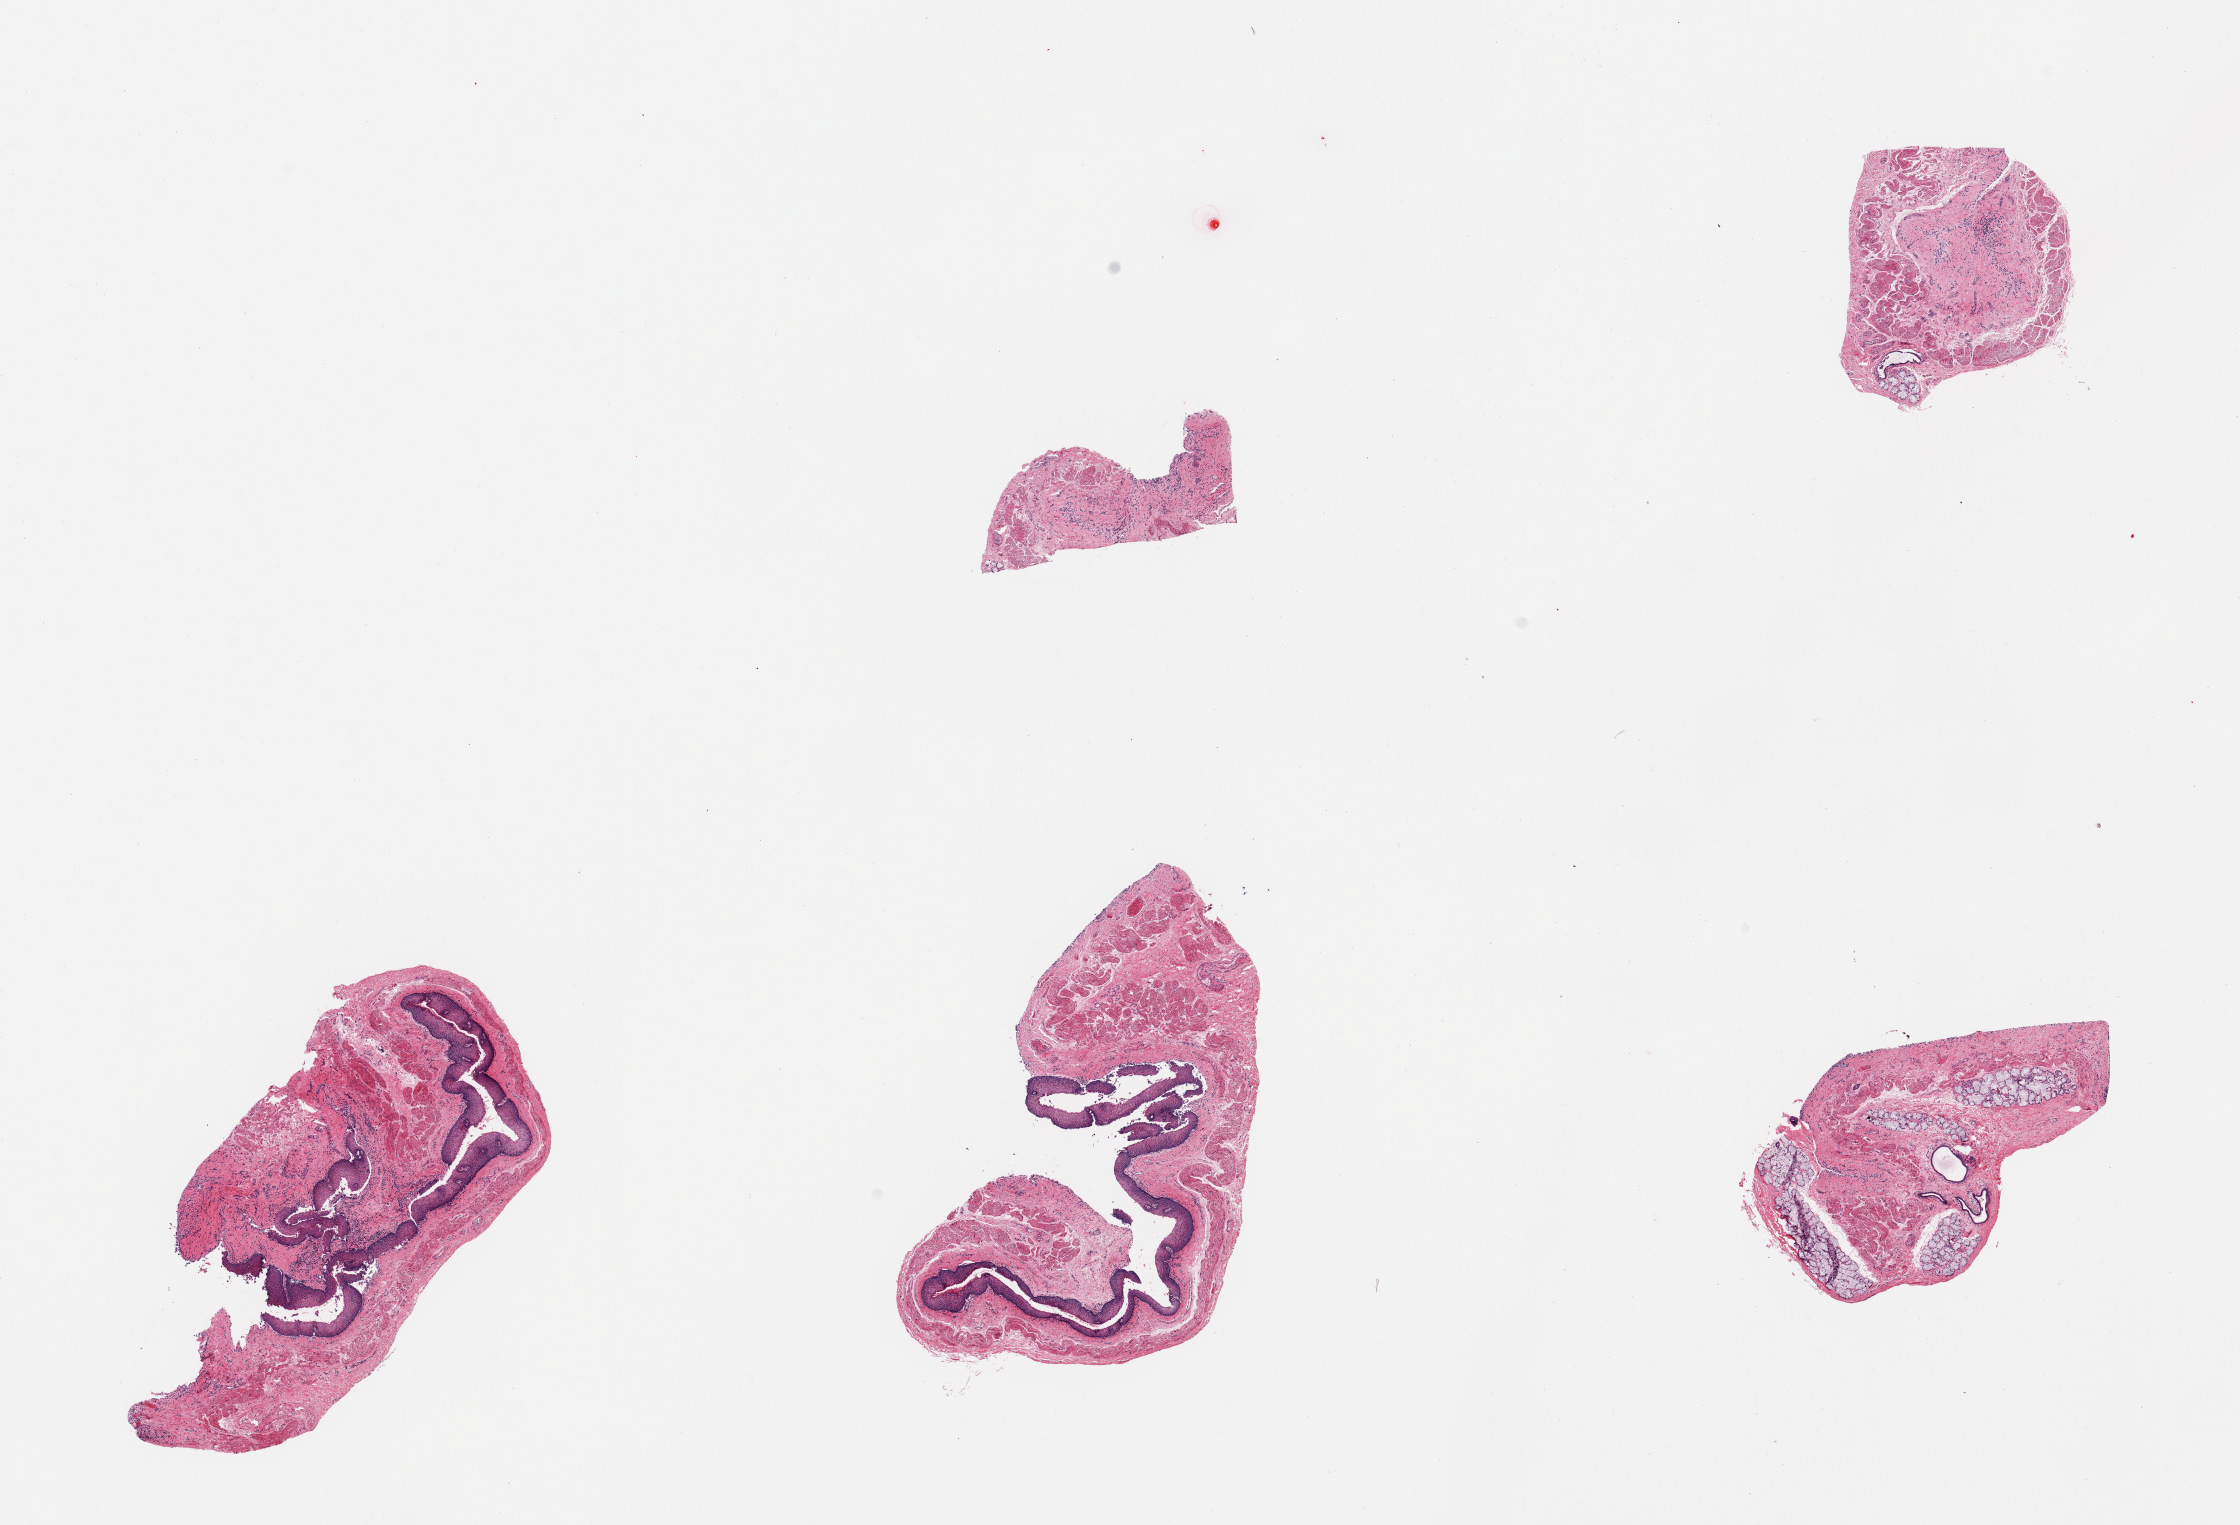
Digitized hematoxylin and eosin (H&E)-stained section — shown as a low-resolution overview of the whole scanned area (about 17.7 x 12.1 mm), PAXgene-fixed paraffin-embedded (PFPE) section, sampled site (target tissue): esophageal mucous membrane, donor tissue sample. Donor: male.
Pathologist's review note for this sample: 5 pieces; only 2 of 5 pieces have epithelium; submucosal glands prominent in 1 piece.